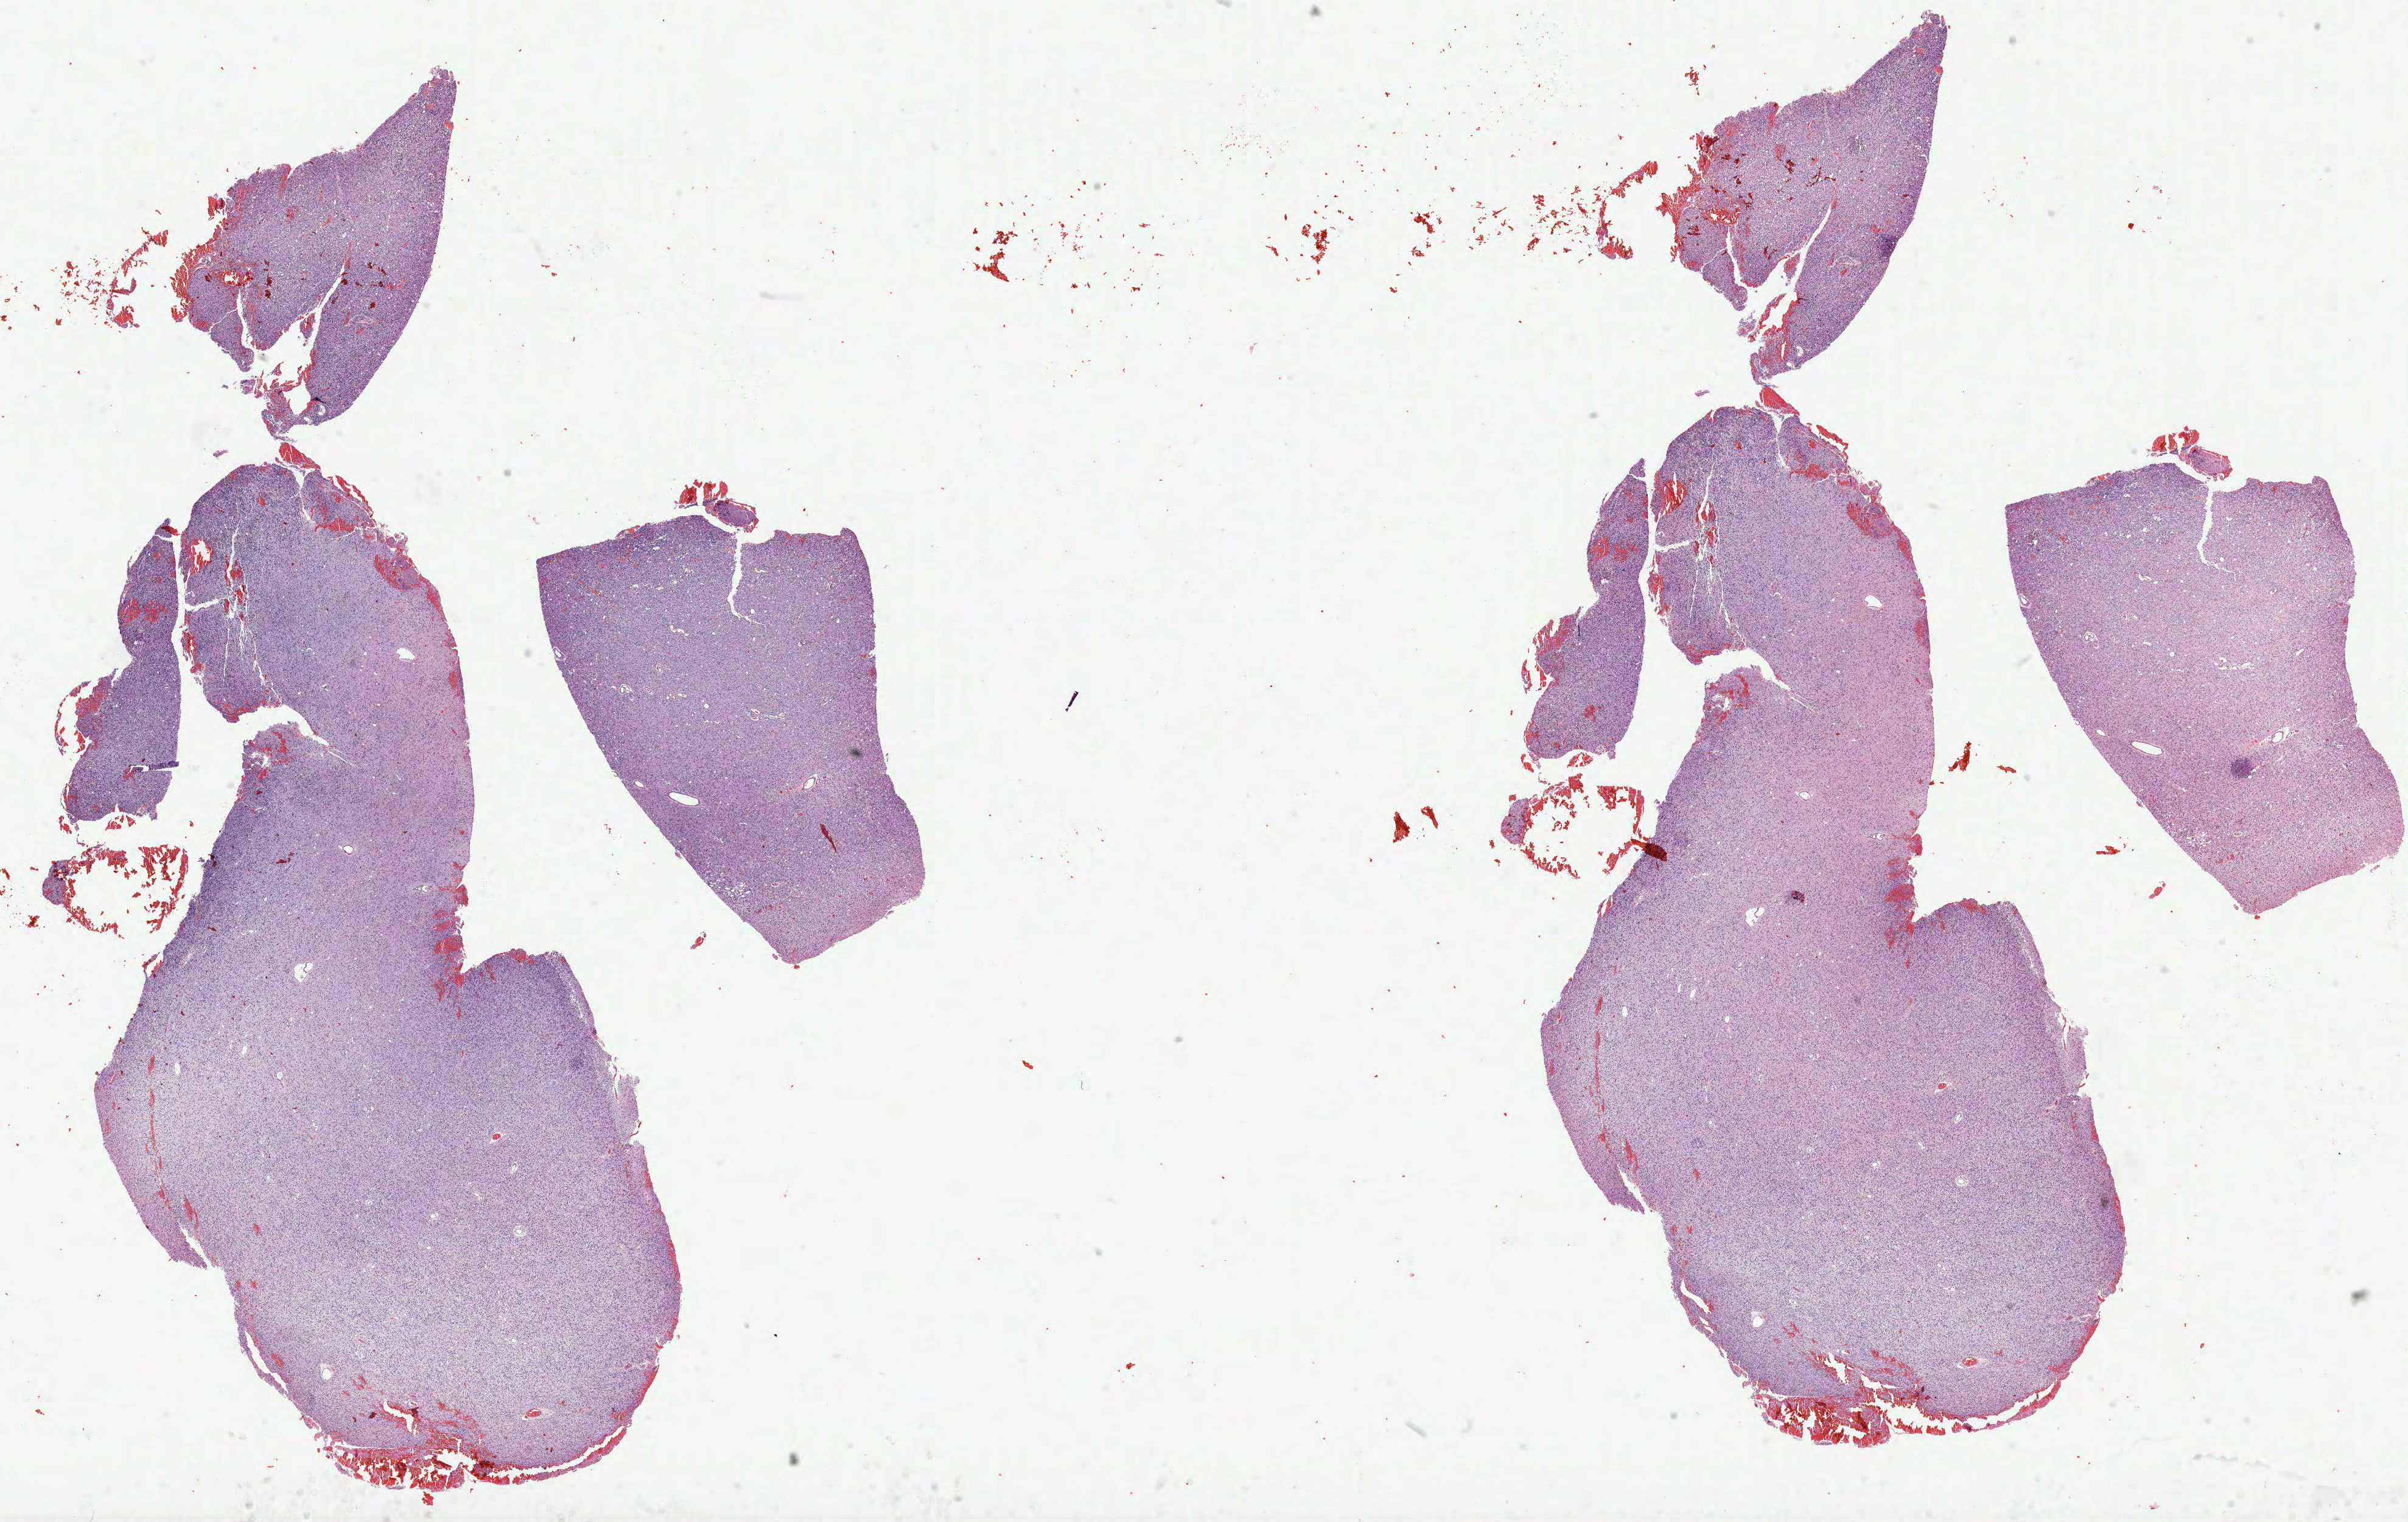
Whole-slide histology image, H&E, a low-resolution overview of the entire scanned area, about 31.9 x 20.2 mm (slide scanned at 40x), formalin-fixed paraffin-embedded (FFPE) diagnostic section, primary tumour sample from the brain. Male, age 48 years at initial diagnosis. Histologic grade: G3 (poorly differentiated).
* diagnosis: Astrocytoma, anaplastic (cerebrum)